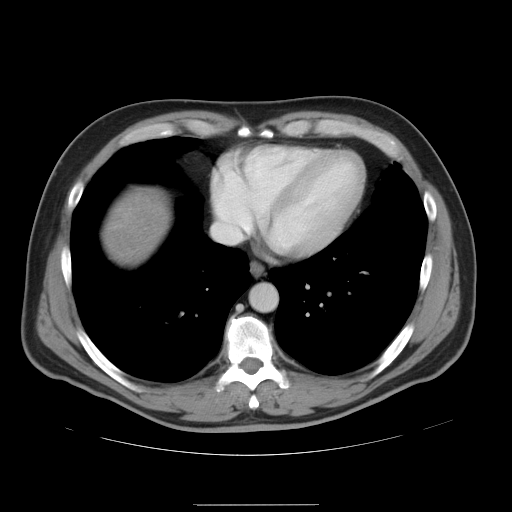
Contrast-enhanced abdominal CT, one axial slice; position 46 of 47 along the scan axis; 120 kVp; intravenous contrast given; soft-tissue window (W 400 / L 40 HU); 5 mm slice thickness; 512 × 512 image matrix, field of view 420 × 420 mm. Male patient, age 61 years. Case-level facts recorded for this patient, not image findings: diagnosis: colorectal cancer liver metastases, imaged before liver resection; multiple liver metastases: no.
Outlined on this slice (expert manual segmentation):
- liver: bounding box (x1, y1, x2, y2) in pixels: (103, 189, 169, 267)
- planned liver remnant (the part of the liver to remain after resection): (103, 189, 169, 267)